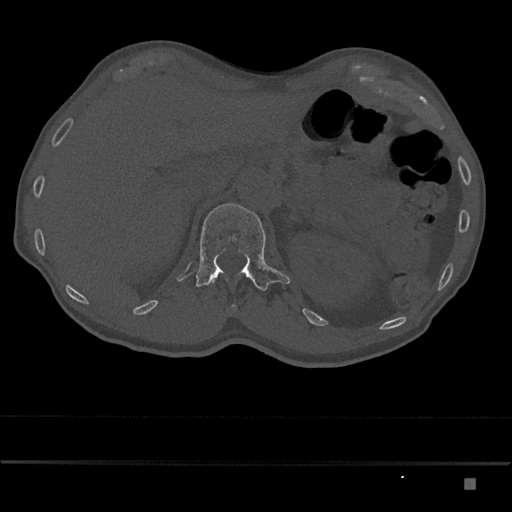
CT including the spine, one axial slice; slice 558 of 797 in the series (ordered by position); reconstruction kernel Br40s/3; bone window (W 1800 / L 400 HU); 512 × 512 image matrix, field of view 390 × 390 mm. Patient: male, 72 years. From the clinical record (not read from this slice): primary cancer: prostate.
Annotated regions visible in this slice (semi-automatic segmentation, software-assisted and operator-edited):
- L1 vertebra: bounding box <196,203,290,291> (left, top, right, bottom; pixels)
- T12 vertebra: <210,278,216,283>